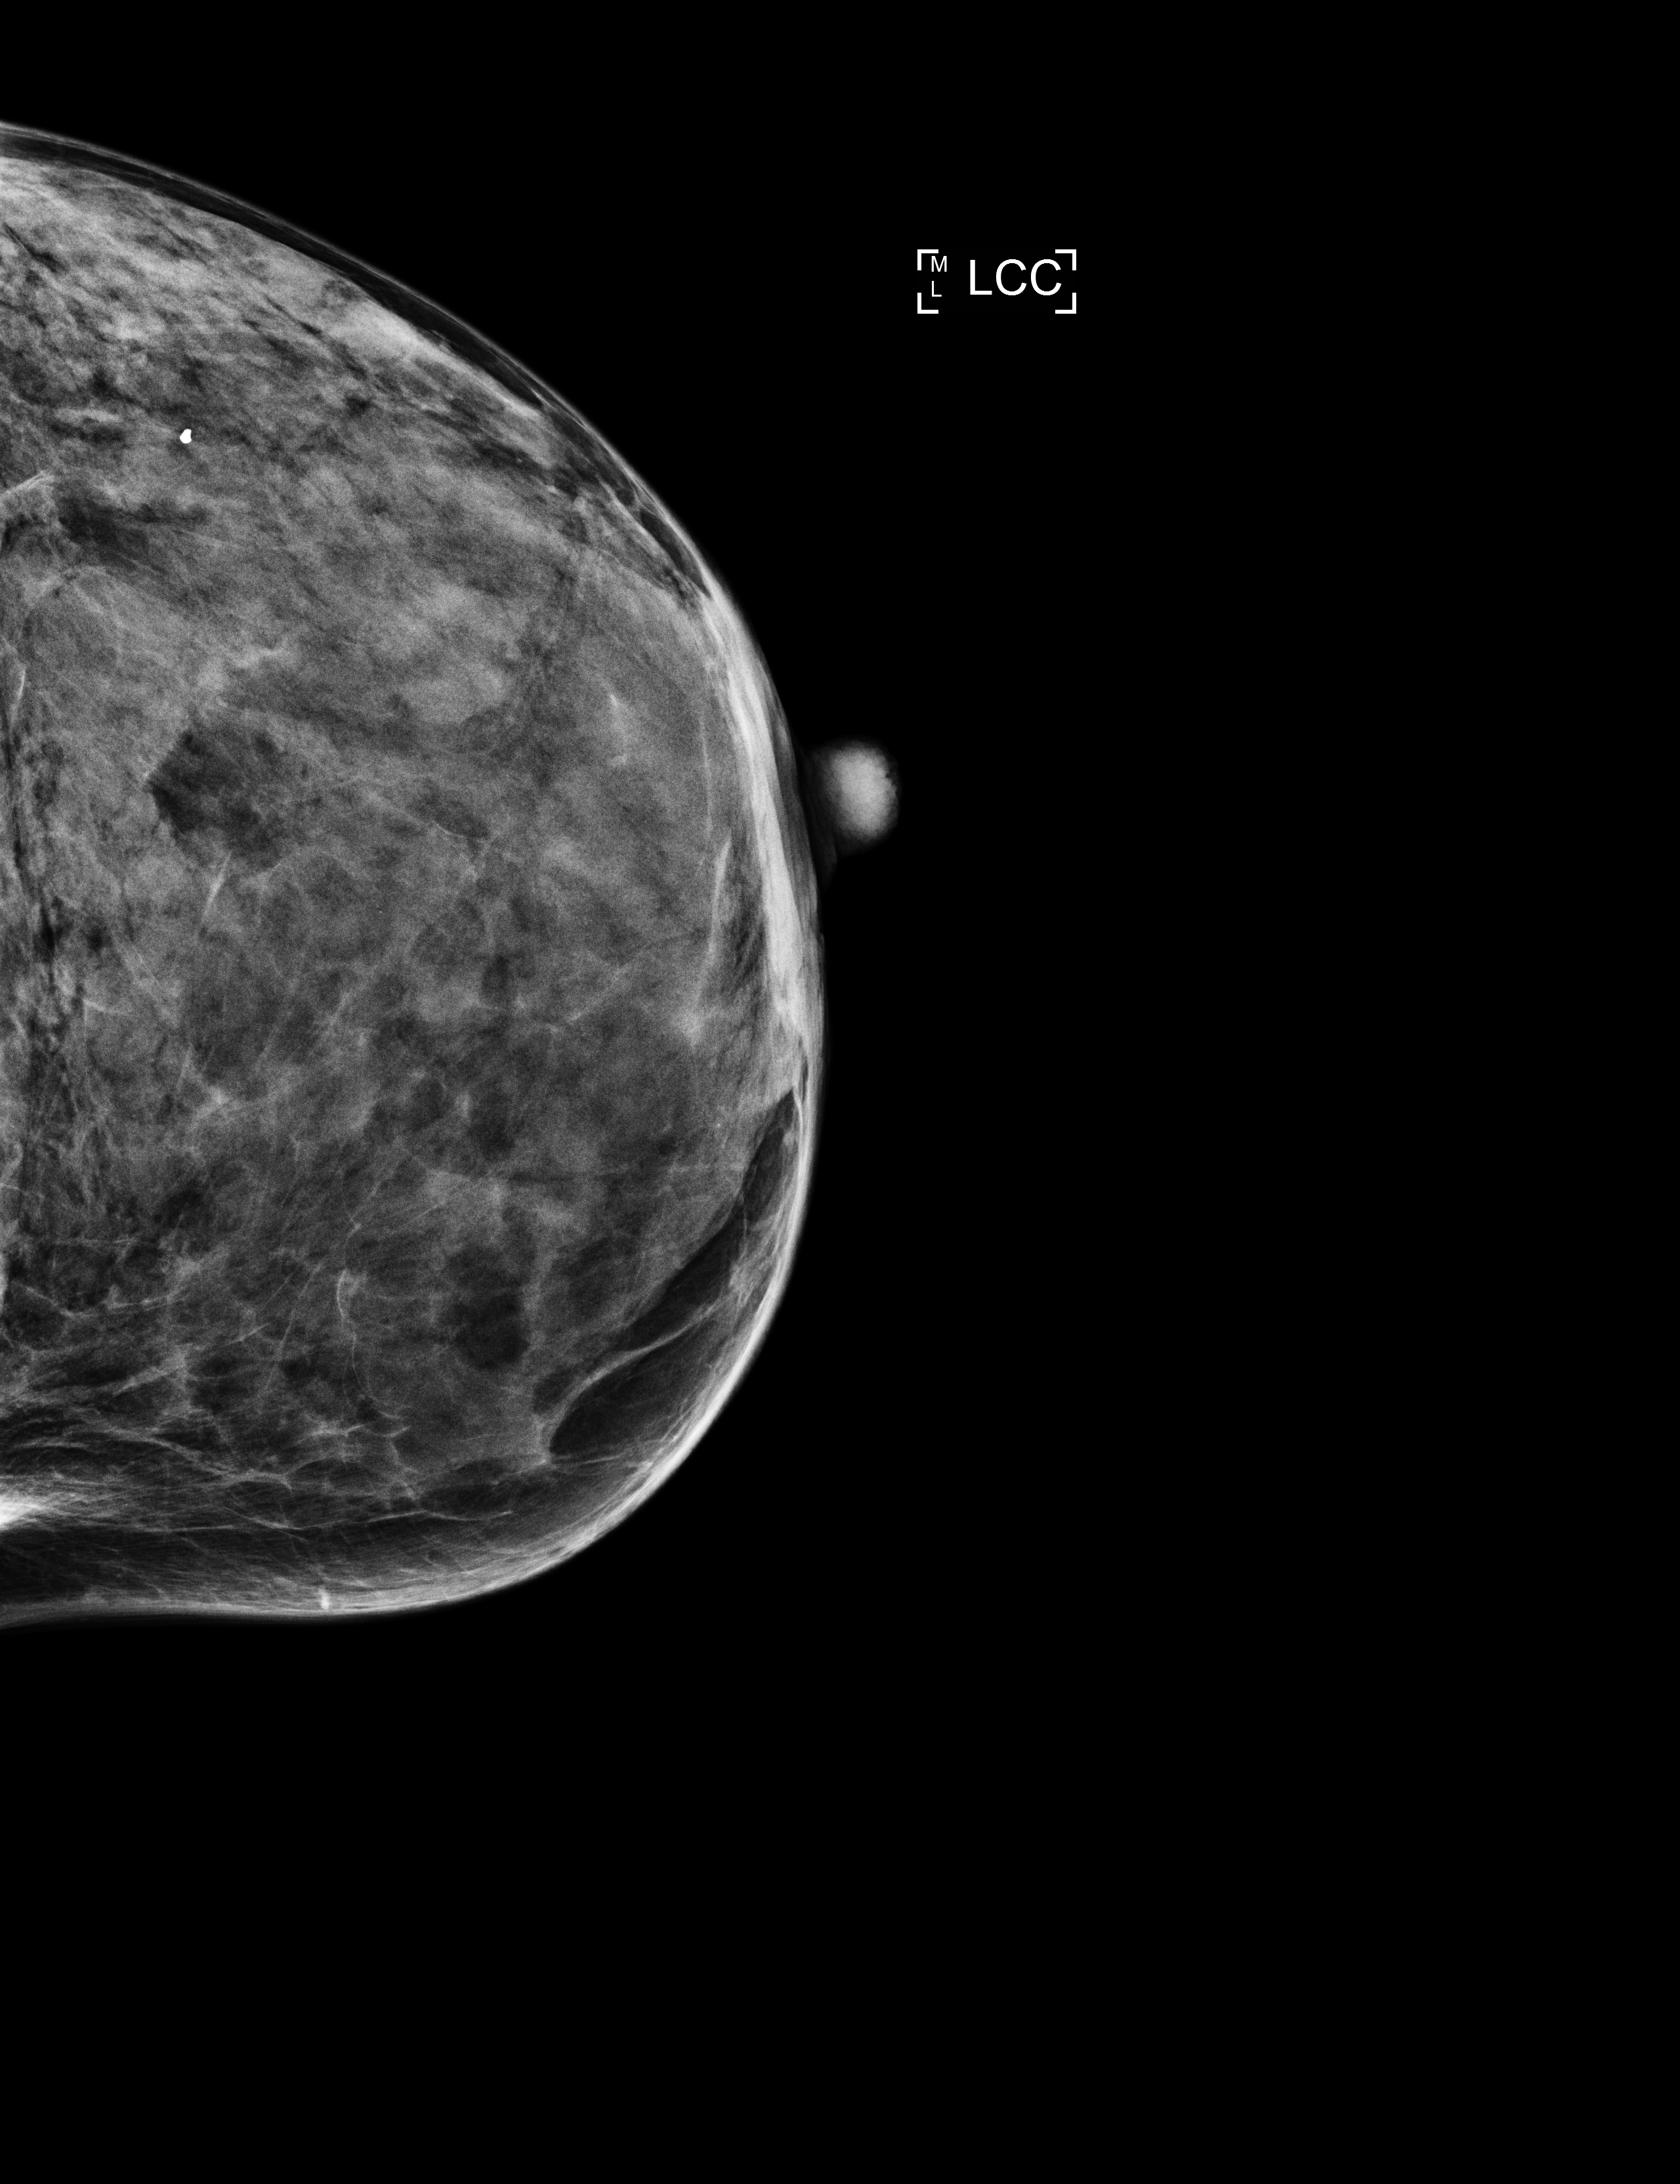
Annual screening mammography examination. Female patient, age 56 years.
Image type: full-field digital mammogram. Breast: left. Projection: cranio-caudal projection.